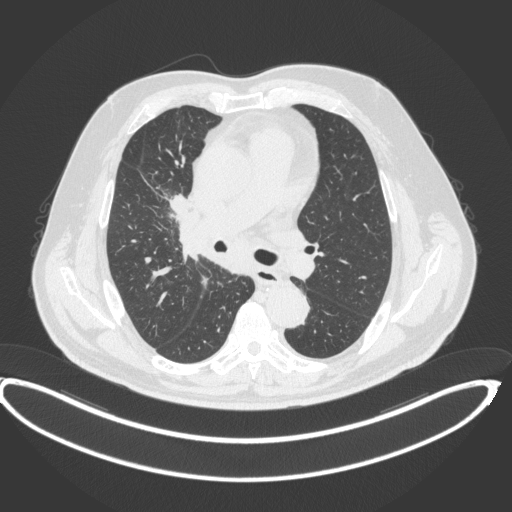
Chest CT, one axial slice. Slice 245 of 395 in the series (ordered by position). 120 kVp. Lung window (W 1500 / L -600 HU). 1 mm slice thickness. 512 × 512 image matrix, field of view 448 × 448 mm. Patient: male, 62 years. Case-level facts recorded for this patient, not image findings: clinical TNM (as recorded): T1c N3 M1c.
Outlined on this slice (rectangle marked by the reading radiologist):
- lung tumour (recorded histology: adenocarcinoma): box from (x=167, y=189) to (x=192, y=216) px